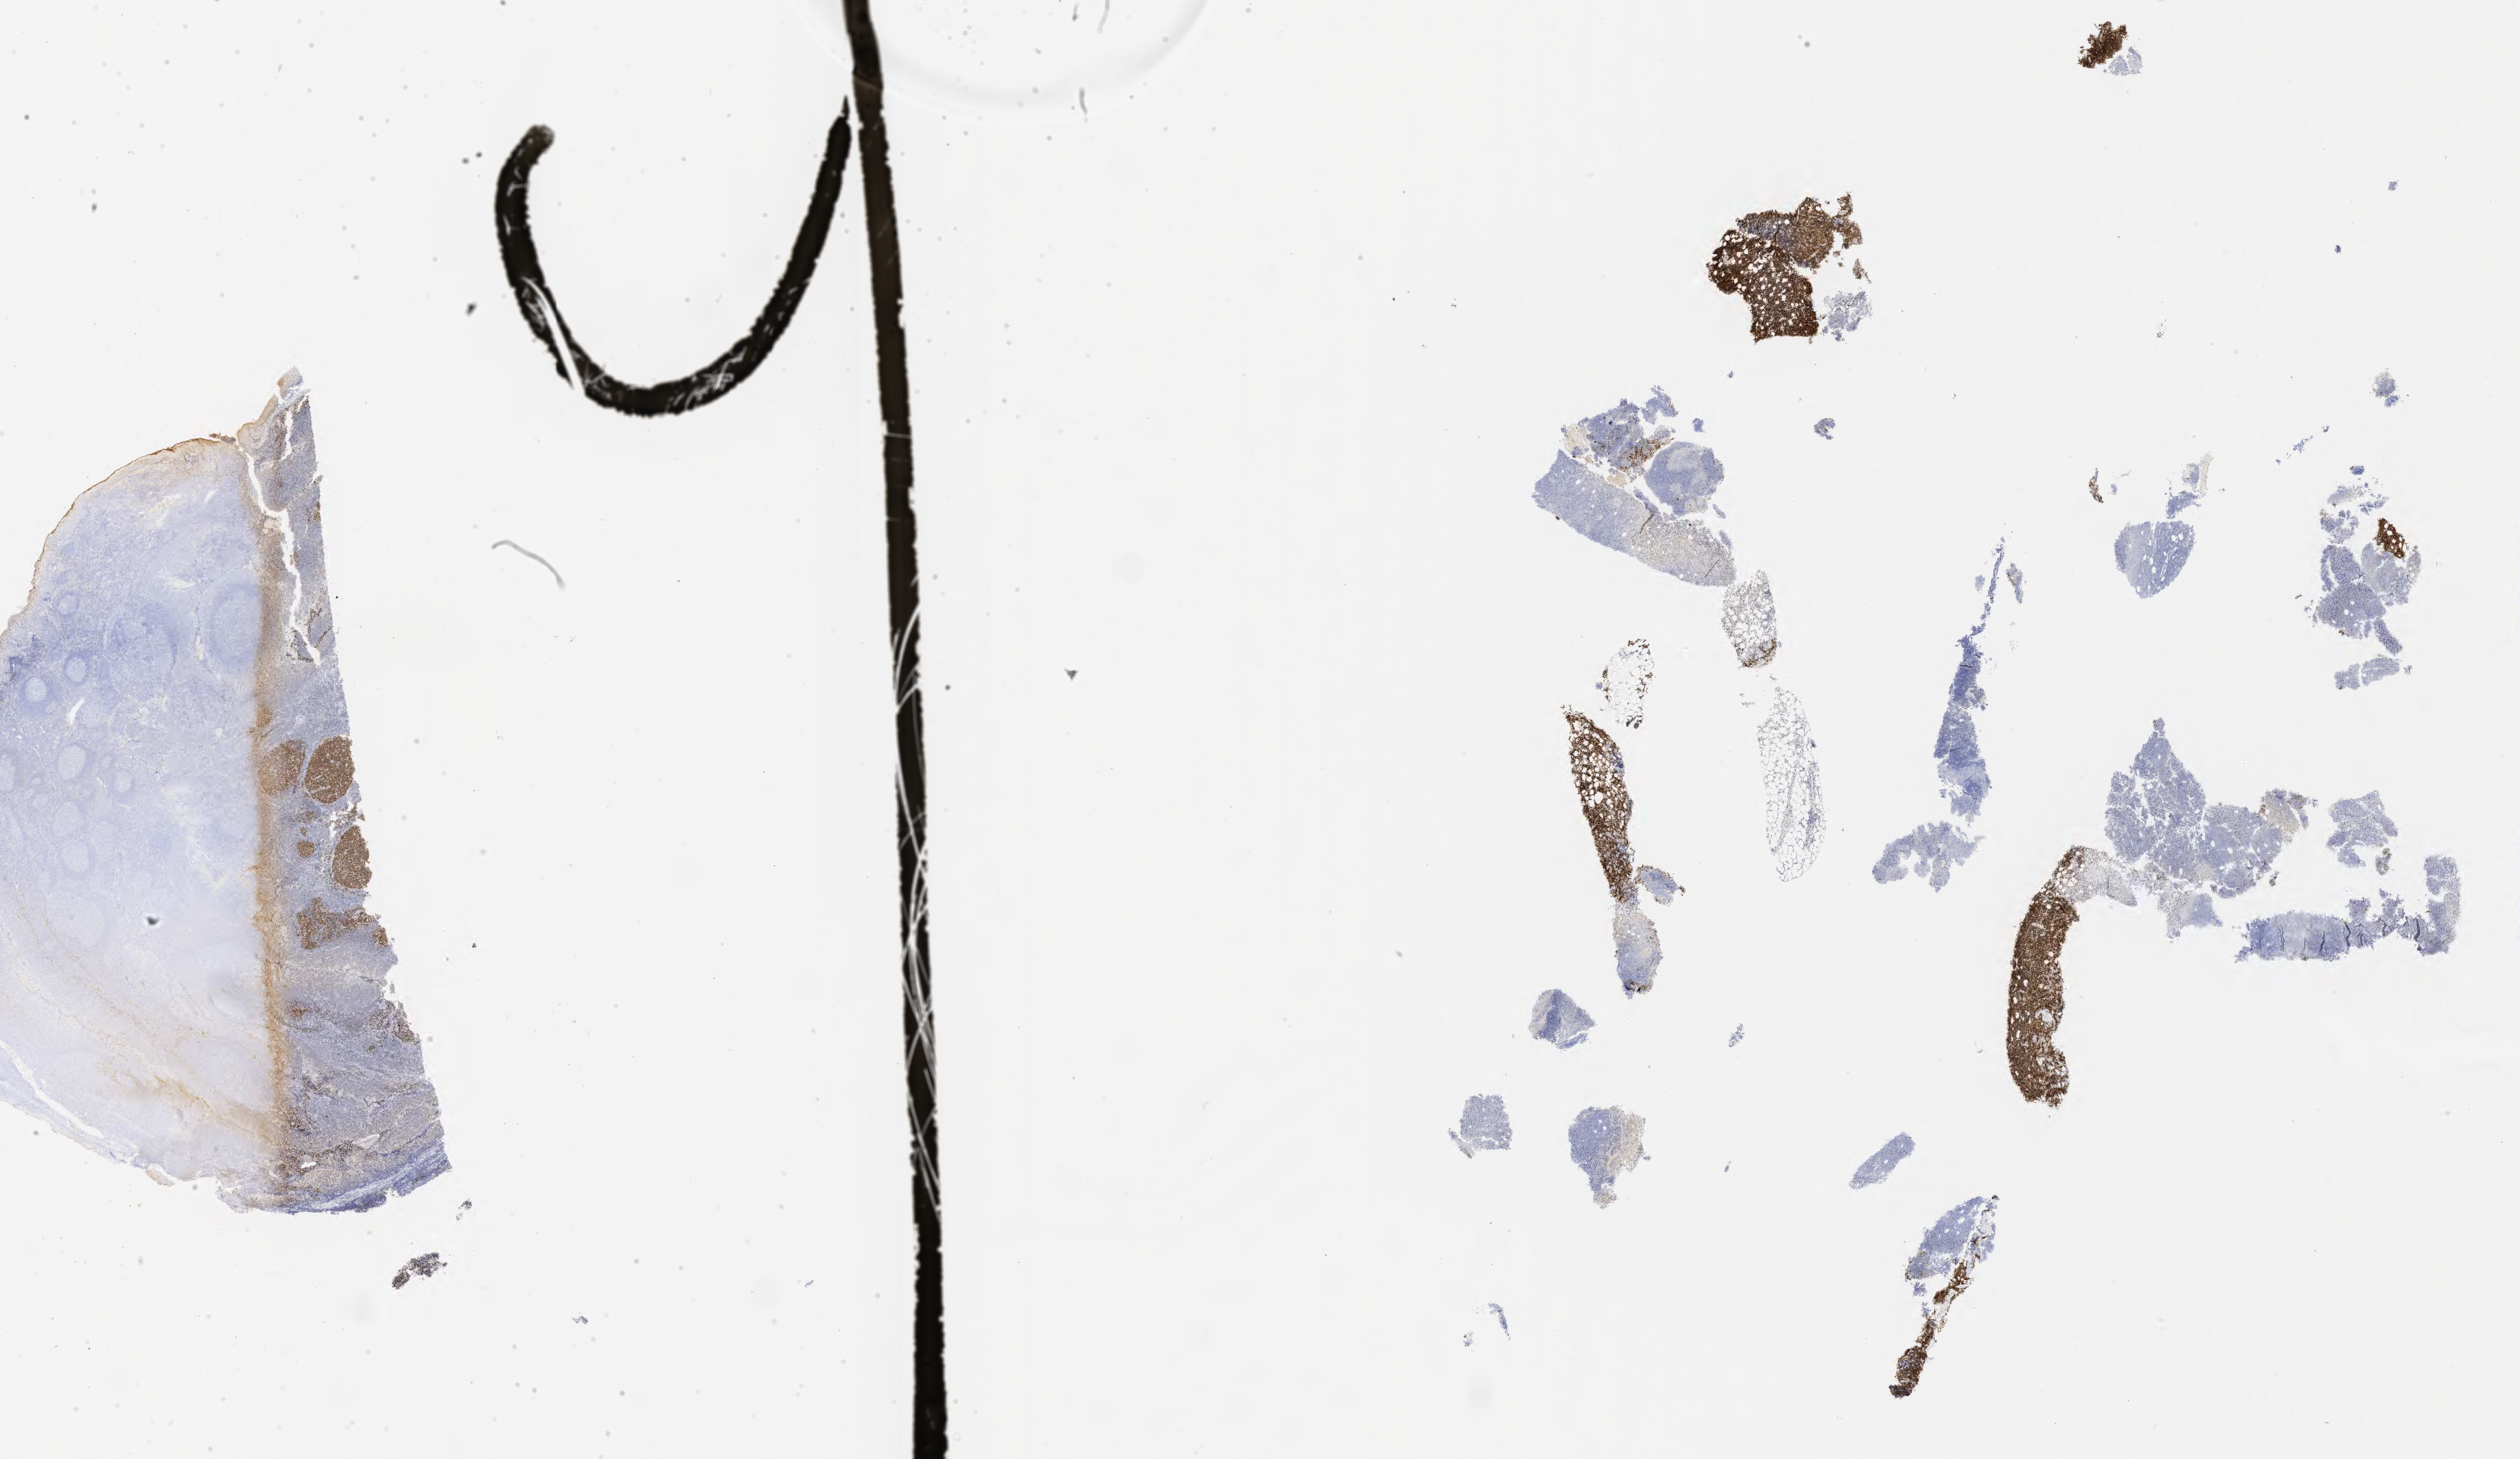
IHC for BCL6, whole-slide image, shown as a low-resolution overview of the whole scanned area (about 29.7 x 17.2 mm); specimen: tumor tissue; anatomic site: pelvis. Patient: female, 64 years old.
* diagnosis: Burkitt lymphoma, NOS